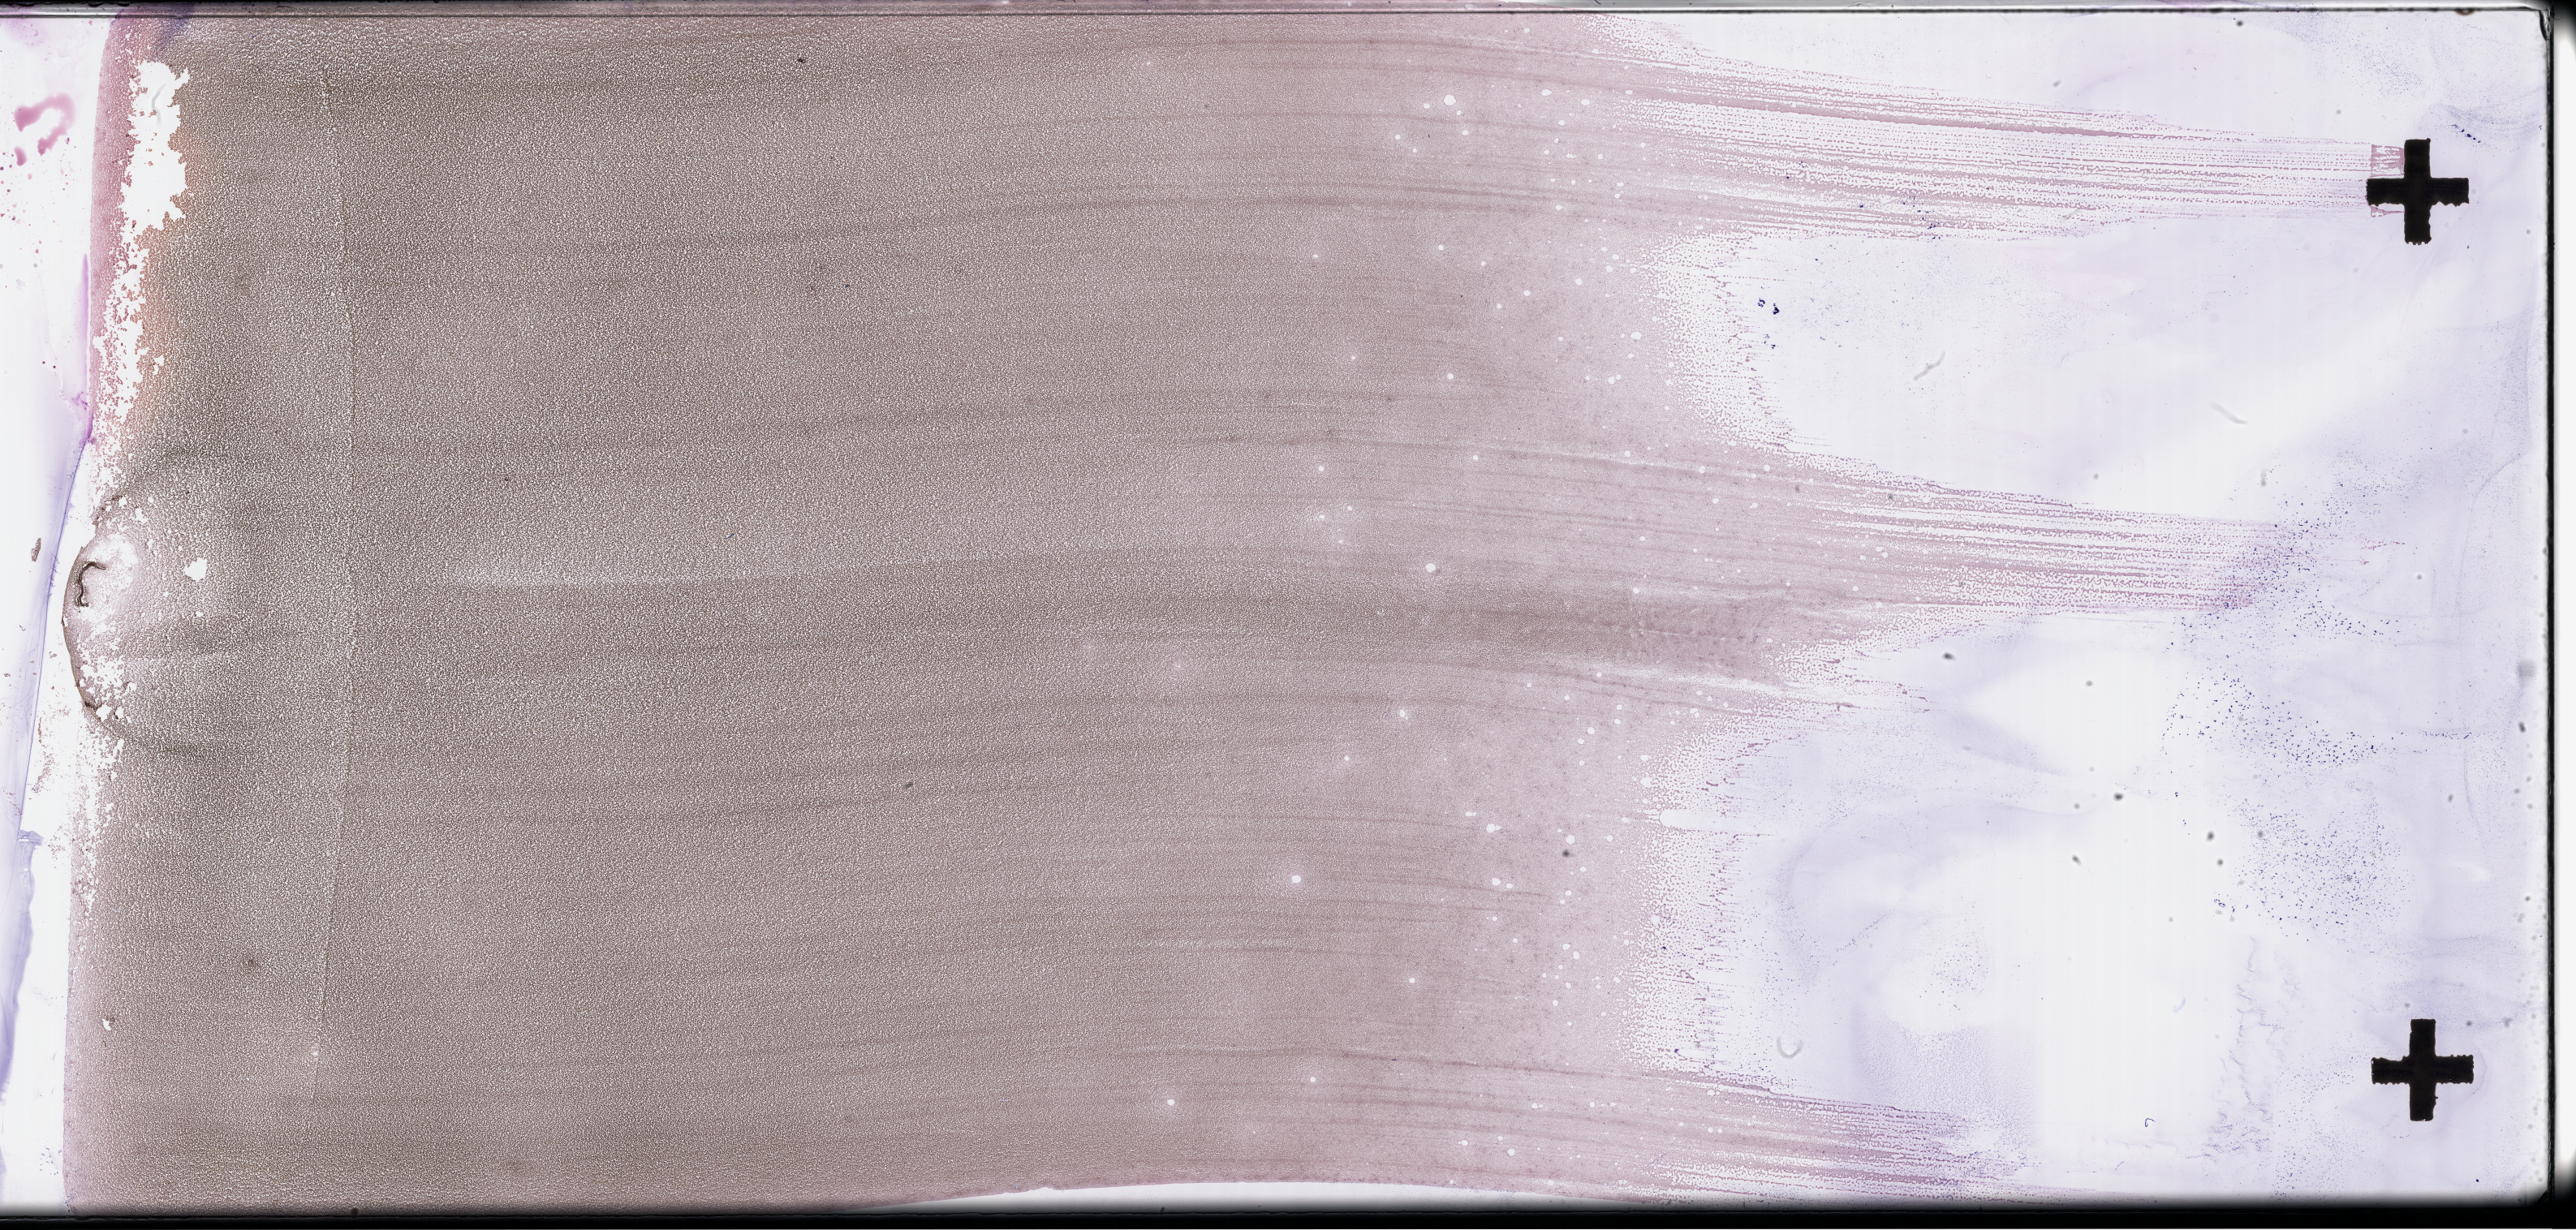
Whole-slide image of a whole blood smear, Wright–Giemsa stain — shown as a low-resolution overview of the whole scanned area (about 51.3 x 24.5 mm); specimen time point: collected on treatment. Patient sex: male.
• patient diagnosis: Plasma Cell Myeloma